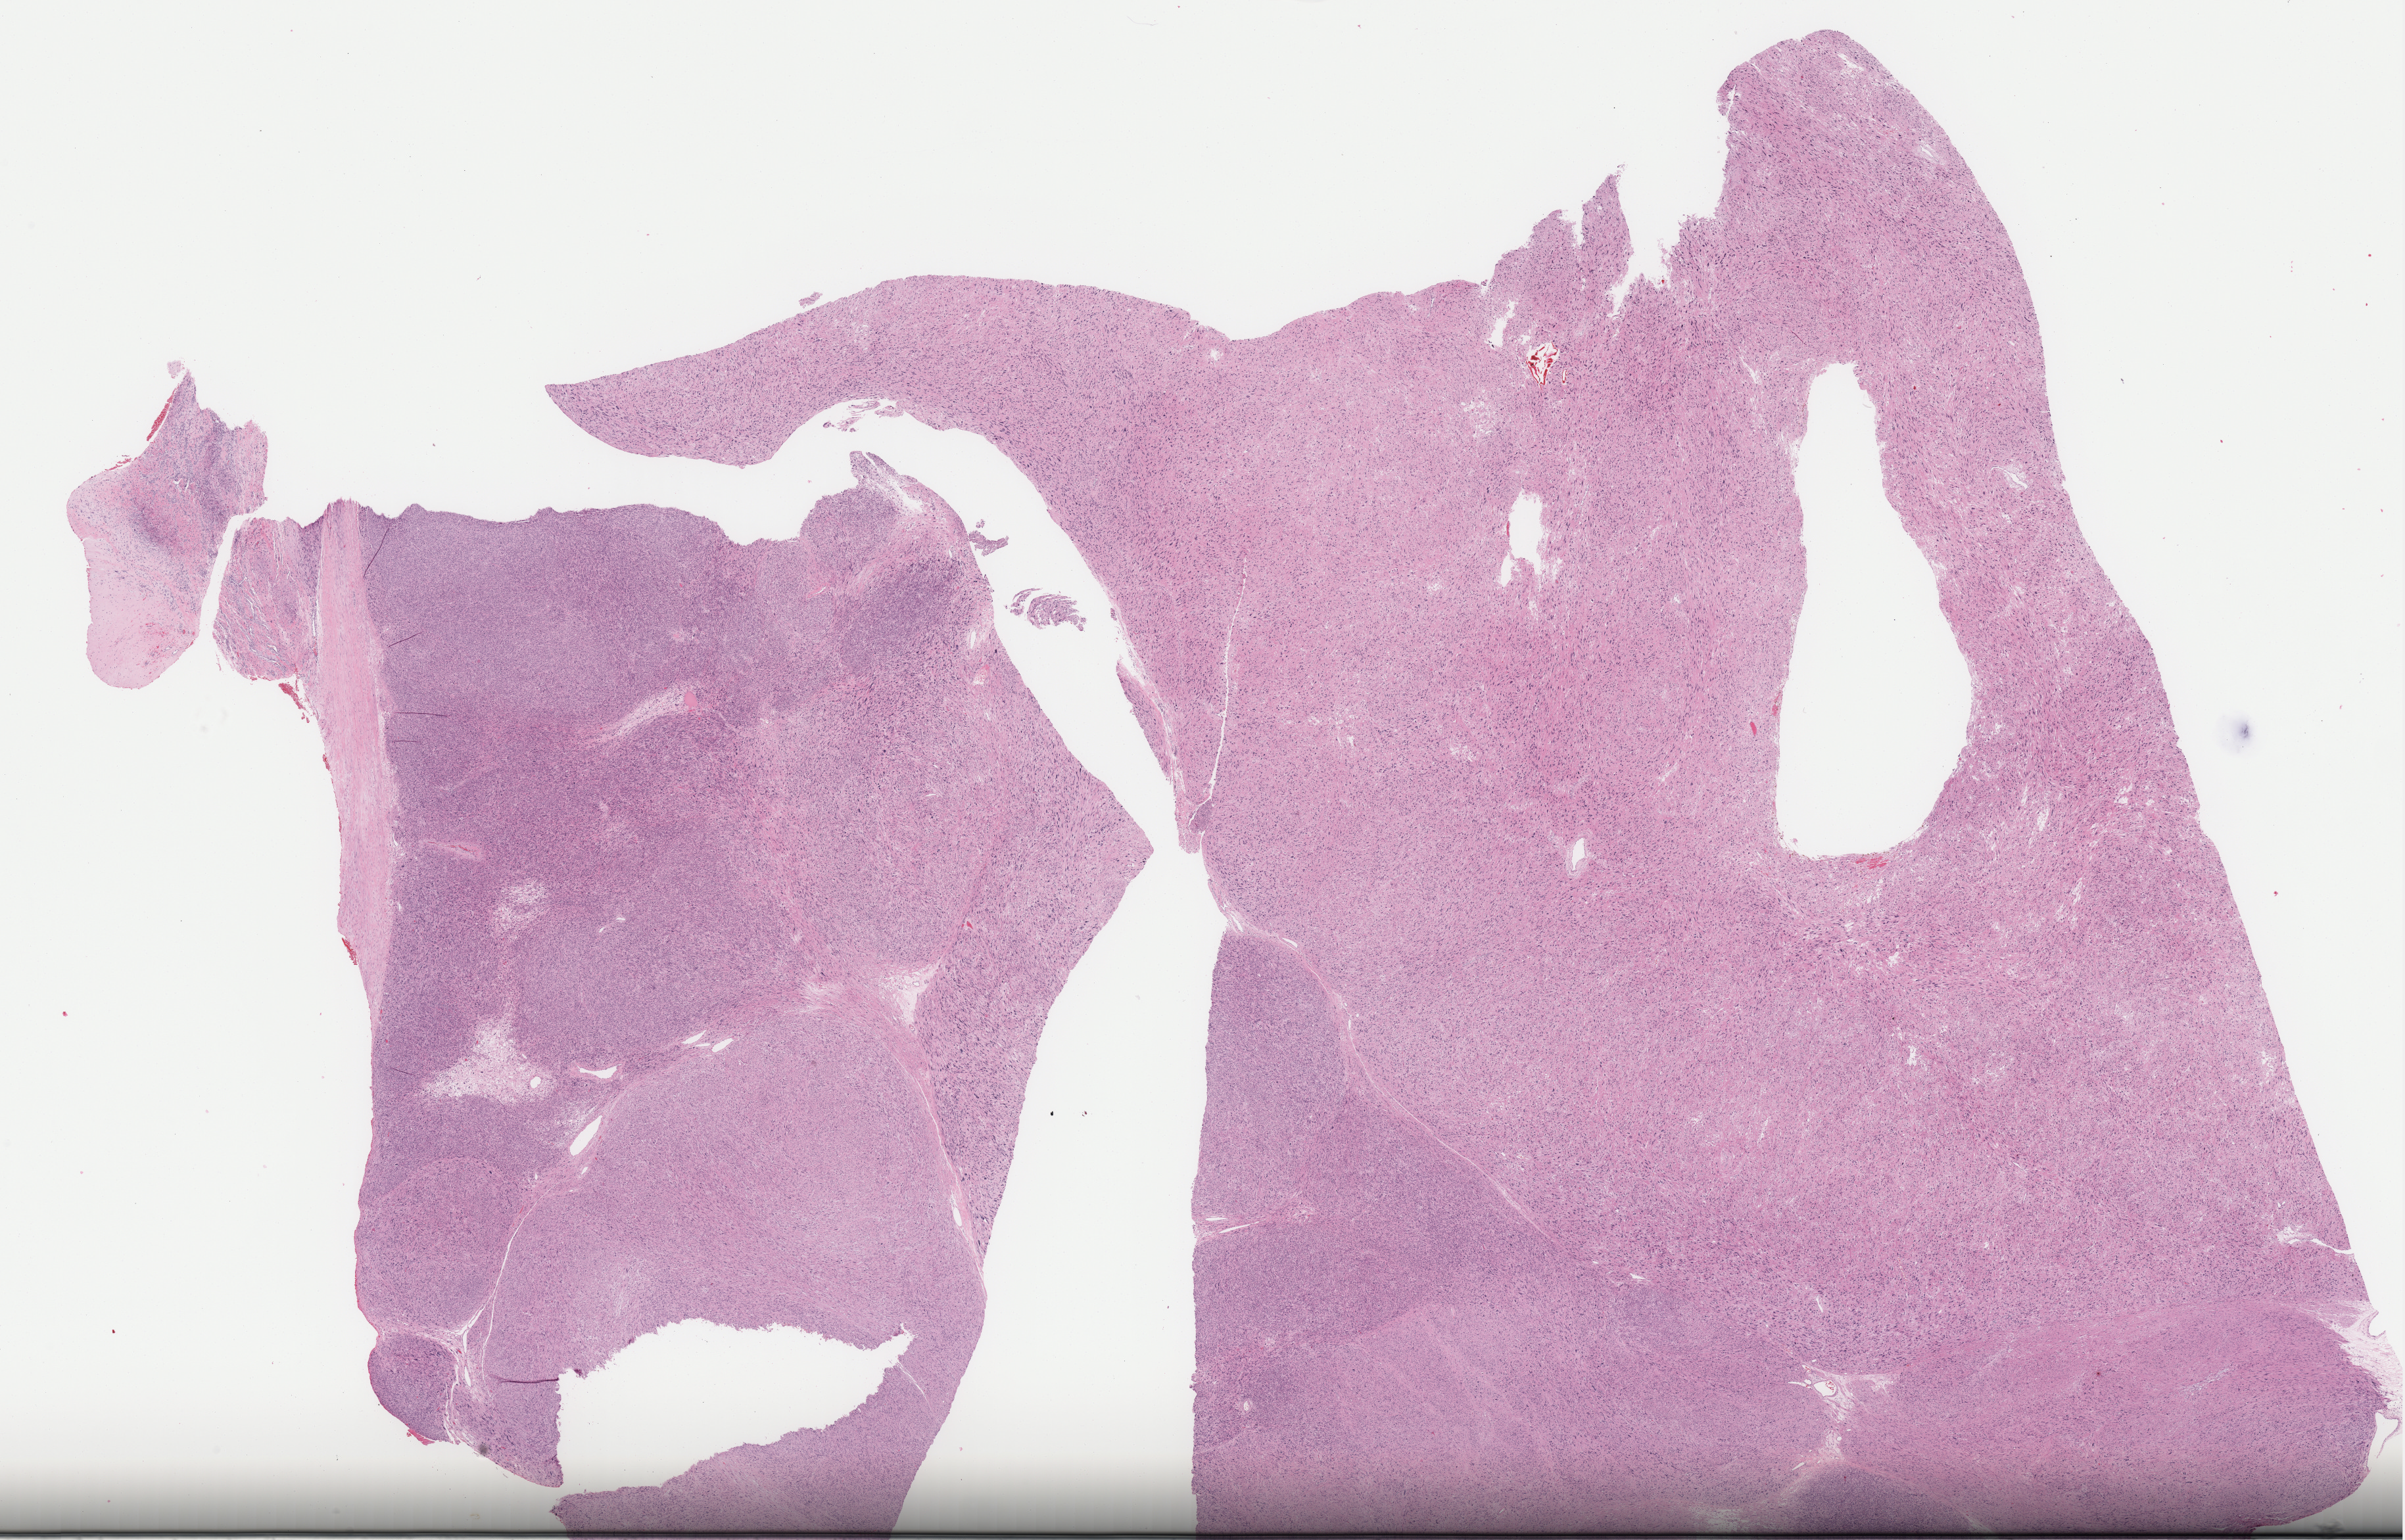
Whole-slide histology image, Hematoxylin and eosin (H&E) stained — low-resolution overview of the scanned area, about 29.2 x 18.7 mm; formalin-fixed paraffin-embedded (FFPE) diagnostic section; sample: primary tumour, retroperitoneum and peritoneum. Patient: male, age at initial diagnosis 55 years.
- pathologic diagnosis: Leiomyosarcoma, NOS